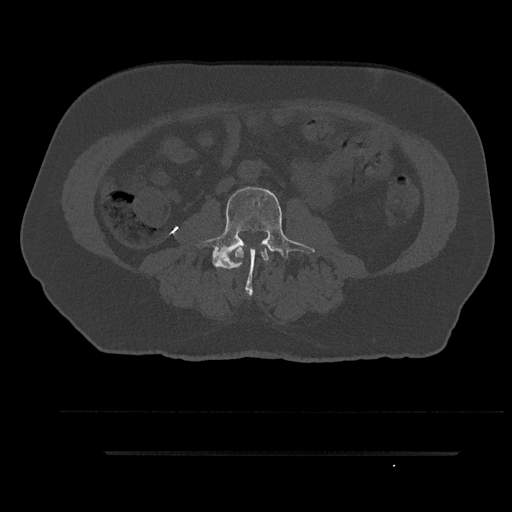
CT including the spine, one axial slice; slice 47 of 797 in the series (ordered by position); reconstruction kernel Br40s/3; 120 kVp; bone window (W 1800 / L 400 HU); 512 × 512 image matrix, field of view 432 × 432 mm. Male patient, age 63 years. Case-level facts recorded for this patient, not image findings: primary cancer: renal; vertebrae with lytic lesions (as recorded): T8.
Annotated regions visible in this slice (semi-automatic segmentation, software-assisted and operator-edited):
- L2 vertebra: bounding box (x1, y1, x2, y2) in pixels: (235, 247, 269, 268)
- L3 vertebra: (197, 185, 315, 295)